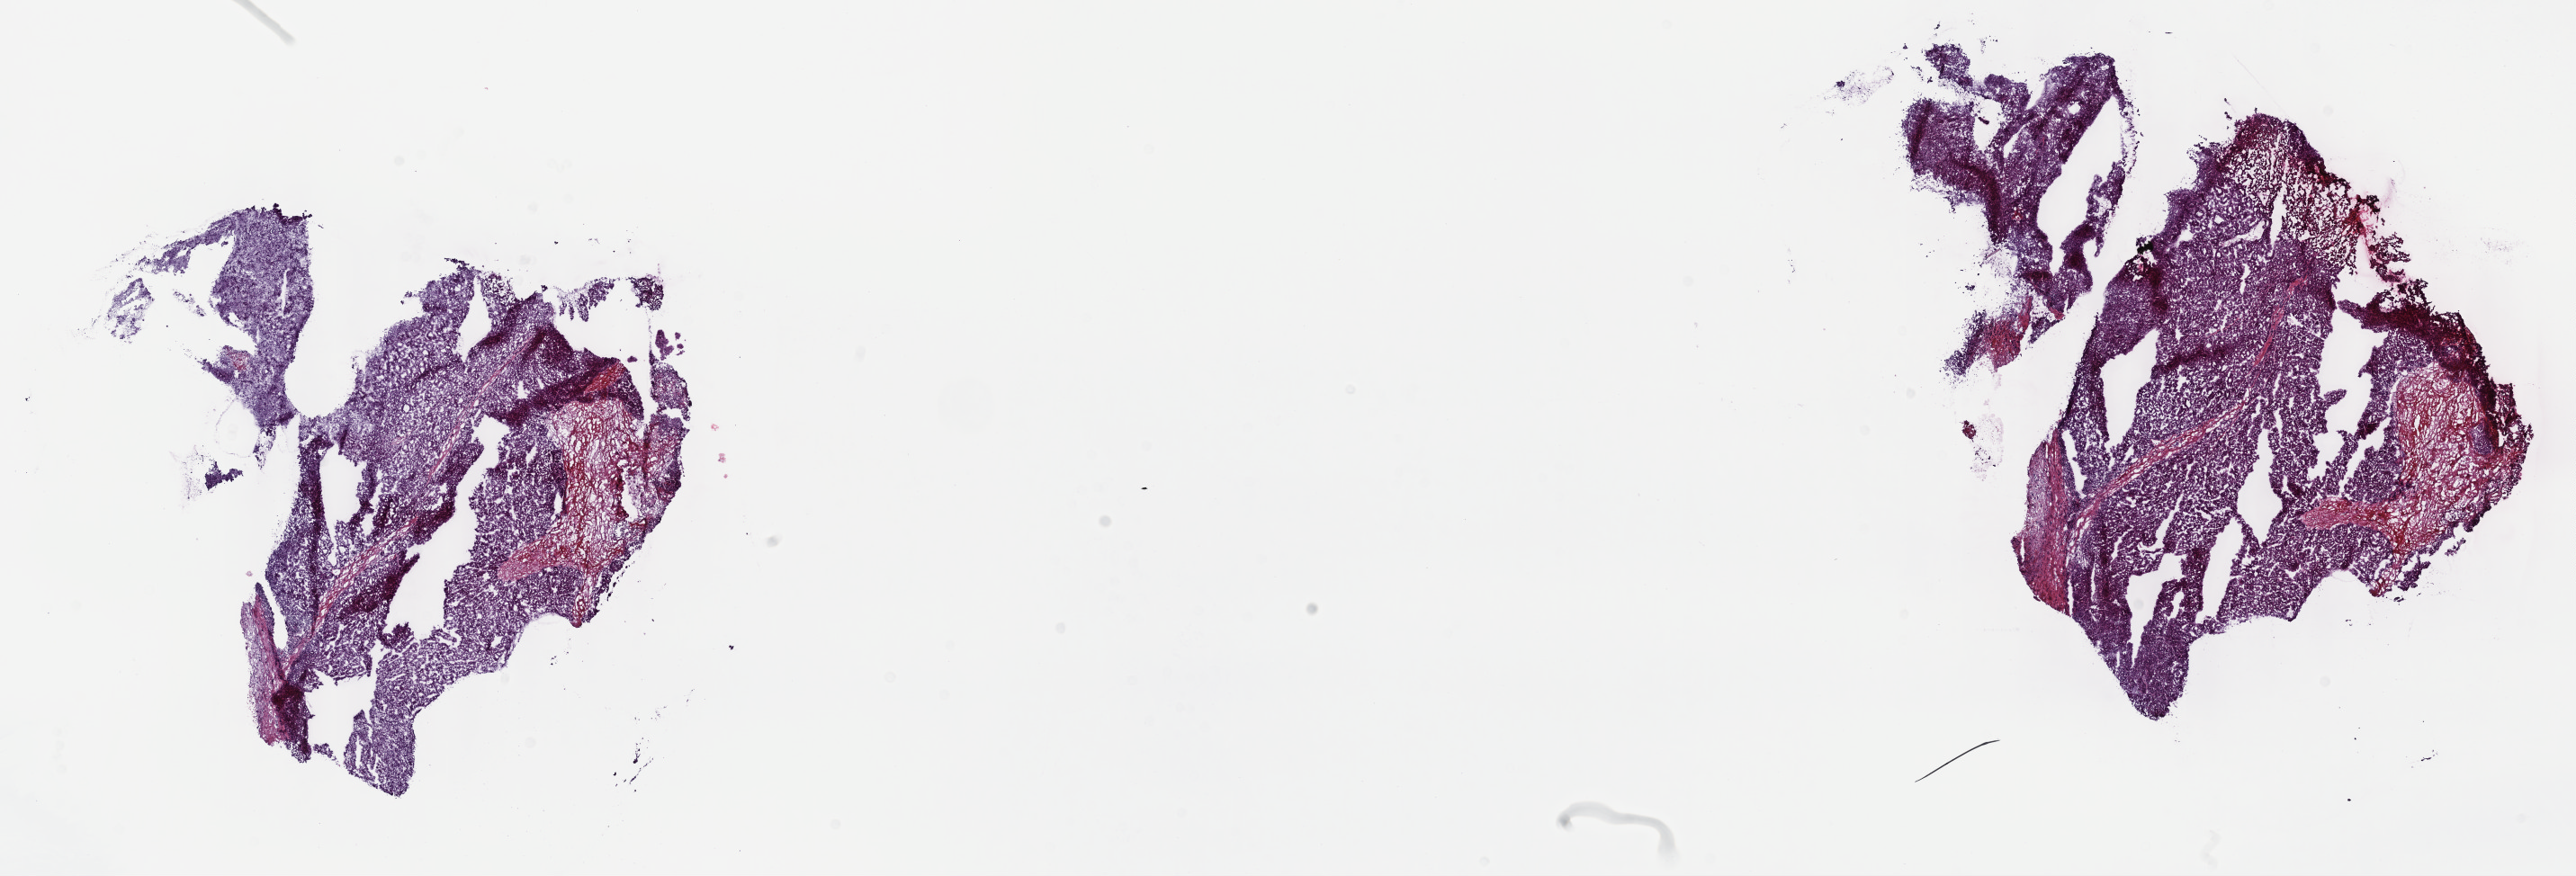
Digitized H&E-stained tissue section (whole slide), shown as a low-resolution overview of the whole scanned area (about 23.2 x 7.9 mm, slide scanned at 40x); frozen section from the top of the tissue portion; sample: primary tumour, liver. Patient: female, age at initial diagnosis 58 years. Histologic grade: G2 (moderately differentiated). Slide review estimates, as recorded: tumour cells 75%, tumour nuclei 75%, normal cells 0%, stromal cells 25%, necrosis 0%. Infiltration values recorded for this section: lymphocyte infiltration 2%, monocyte infiltration 0%, neutrophil infiltration 0%.
TNM: T2 N0 M0. Diagnosis: Hepatocellular carcinoma, NOS. AJCC pathologic stage: II (7th edition).